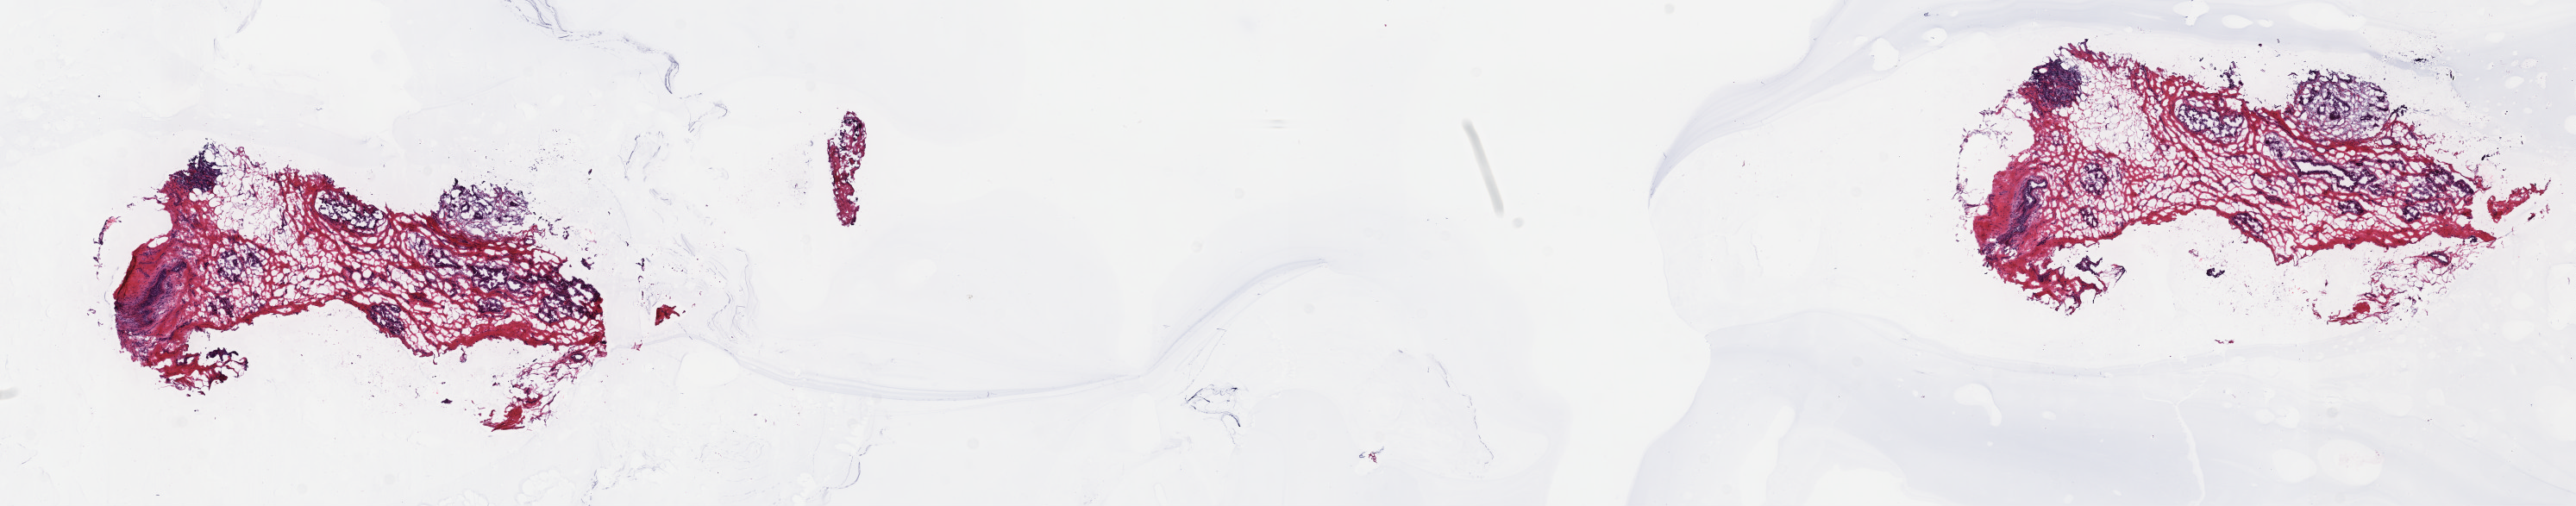
H&E-stained whole-slide image — whole scanned area (about 24.2 x 4.7 mm) shown as a low-resolution overview. FFPE section. Primary tumour sample from the breast. Female patient; age at initial diagnosis 54 years.
Diagnosis: Medullary carcinoma, NOS.